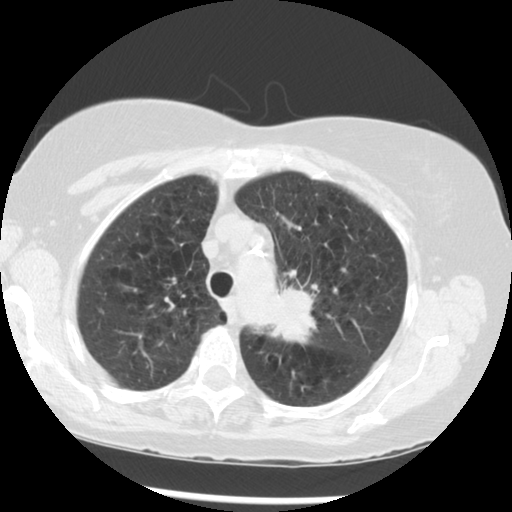
Chest CT (low-dose screening protocol), one axial image, third annual screen, lung window (W 1500 / L -600 HU), 2.5 mm slice thickness, standard (soft-tissue) reconstruction kernel (STANDARD), slice 219 of 283 in the series, 512 × 512 image matrix. Female participant, aged 70 years at enrolment.
Expert-annotated lung lesion, box from (x=263, y=271) to (x=358, y=360) px. Reader record for this screening exam (exam-level; its link to the box is not recorded): non-calcified nodule or mass ≥4 mm, left upper lobe, 32 × 26 mm, spiculated (stellate) margins, soft tissue attenuation, pre-existing on the prior screen: yes; interval growth: yes. Lung cancer was diagnosed 24 days after this screen: neoplasm, malignant, left upper lobe, stage IIIB (AJCC 6th edition), 40 mm at pathology.